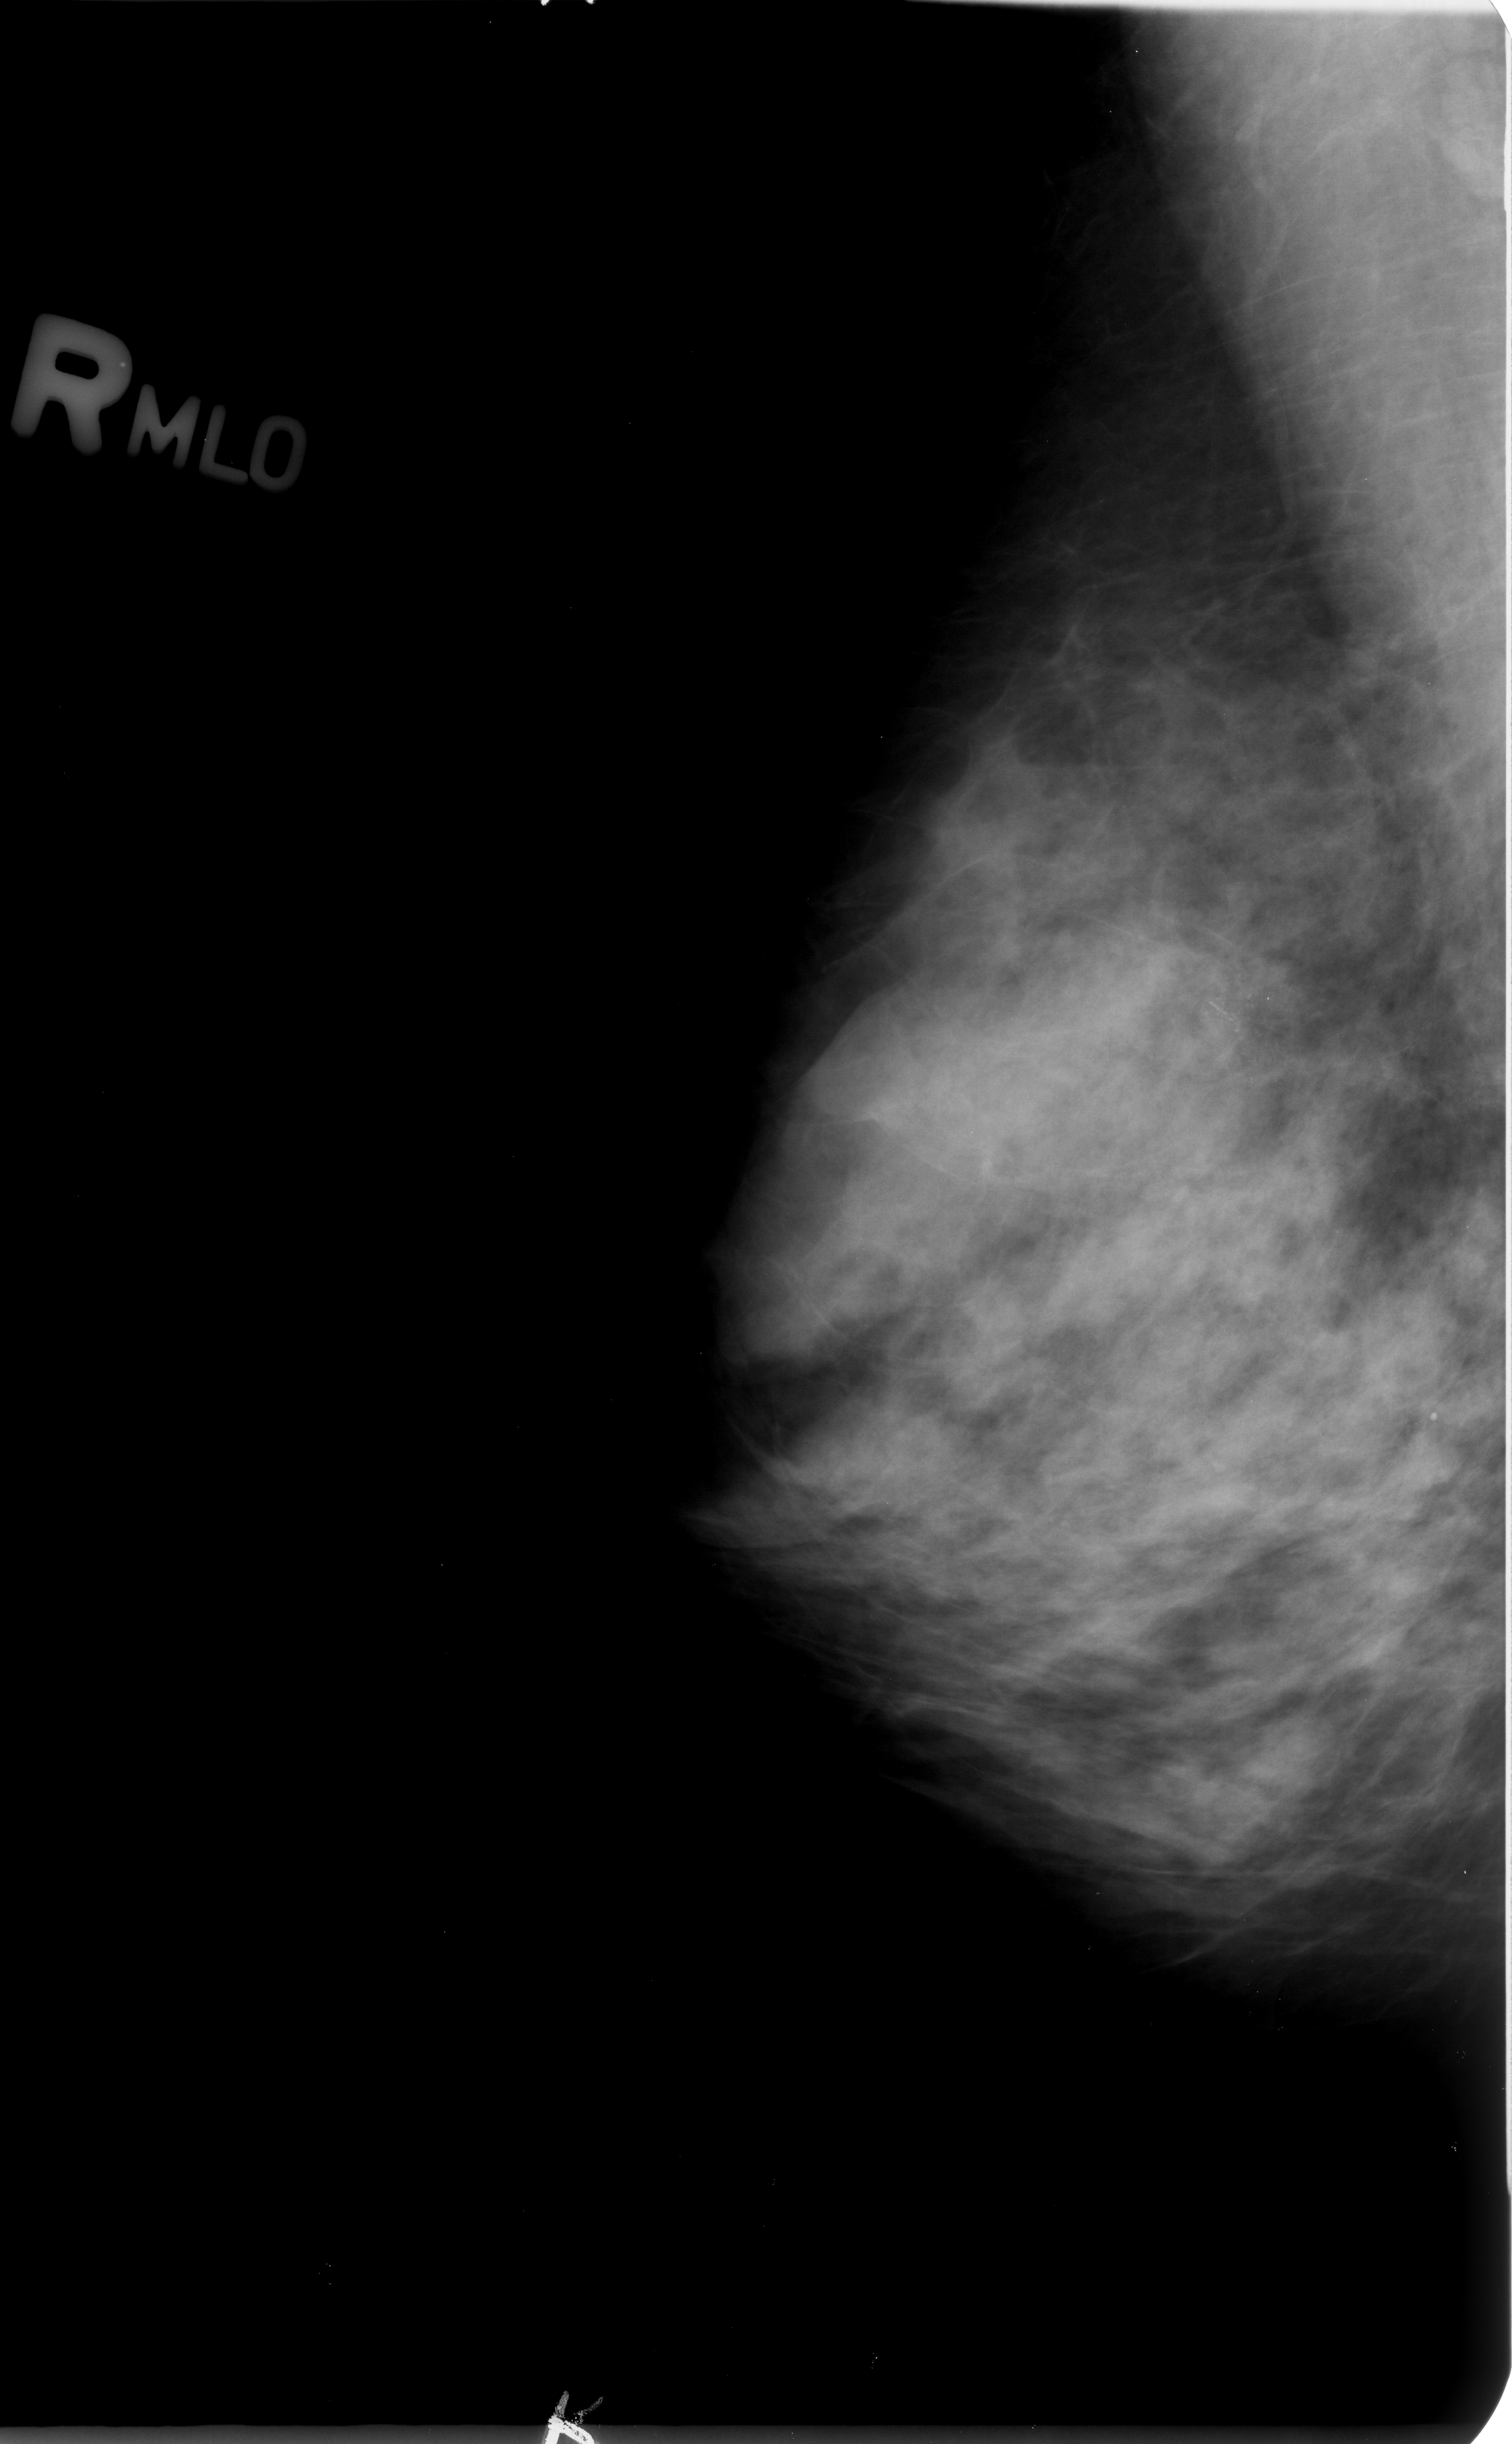
Scanned film-screen mammogram, right breast, MLO view, BI-RADS breast density category 4 (scale 1–4).
- Marked abnormality: calcifications, morphology pleomorphic, distribution clustered; BI-RADS assessment category 4; subtlety rating 4 on a 1 (subtle) to 5 (obvious) scale; pathology result (as recorded, not read from the image): malignant.